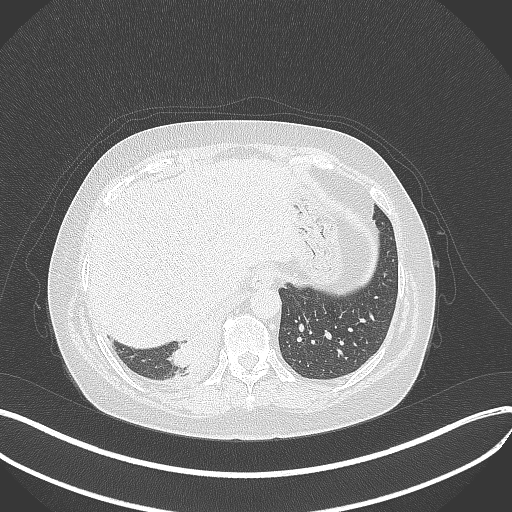
Chest CT, one axial slice. Position 79 of 381 along the scan axis. 120 kVp. Lung window (W 1500 / L -600 HU). 1 mm slice thickness. 512 × 512 image matrix, field of view 400 × 400 mm. Patient: female, 56 years. From the clinical record (not read from this slice): clinical TNM (as recorded): T2b N1 M0; histopathological grade: G3.
Outlined on this slice (rectangle marked by the reading radiologist):
- lung tumour (recorded histology: small cell carcinoma): bounding box <169,334,222,371> (left, top, right, bottom; pixels)